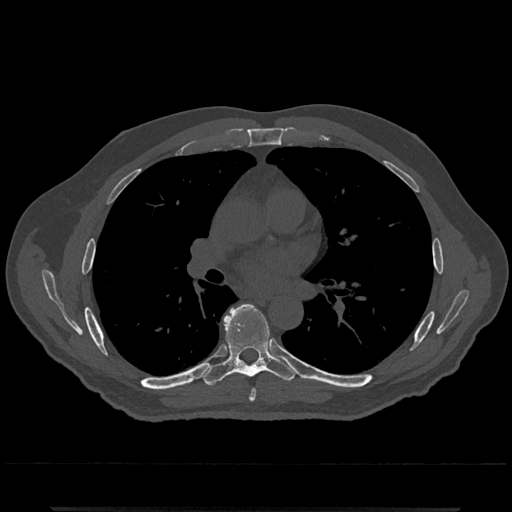
CT including the spine, one axial slice. Position 732 of 797 along the scan axis. Reconstruction kernel Br40s/3. Bone window (W 1800 / L 400 HU). 0.5 mm slice thickness. 512 × 512 image matrix. Patient: male, 67 years. From the clinical record (not read from this slice): primary cancer: prostate.
Outlined on this slice (semi-automatic segmentation, software-assisted and operator-edited):
- T6 vertebra: bounding box <249,391,256,402> (left, top, right, bottom; pixels)
- T7 vertebra: <204,304,297,386>